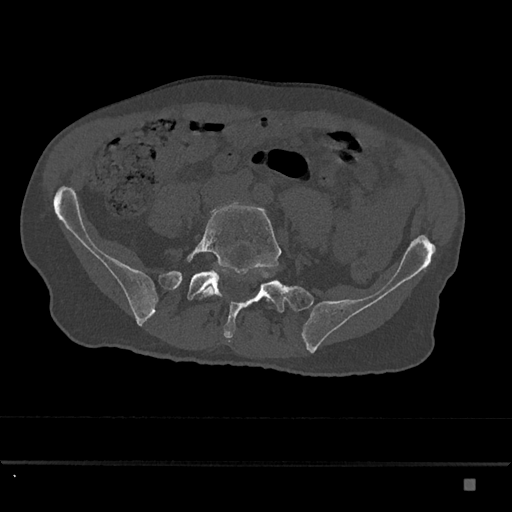
CT including the spine, one axial slice. Position 258 of 797 along the scan axis. Bone window (W 1800 / L 400 HU). 0.5 mm slice thickness. 512 × 512 image matrix, field of view 390 × 390 mm. Patient: male, 72 years. From the clinical record (not read from this slice): primary cancer: prostate.
Outlined on this slice (semi-automatic segmentation, software-assisted and operator-edited):
- L5 vertebra: box from (x=187, y=204) to (x=282, y=299) px